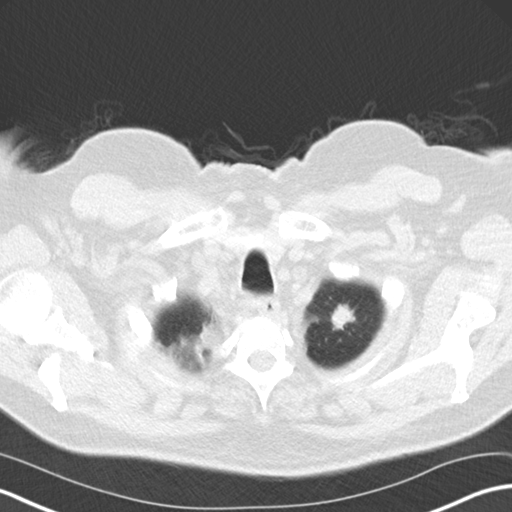
Axial slice from a low-dose chest CT screening exam. Third screening round (two years after baseline). Lung window (W 1500 / L -600 HU). 5 mm slice thickness. Standard (soft-tissue) reconstruction kernel (B30f). 512 × 512 image matrix. Male participant, aged 67 years at enrolment.
- Lesion marked by an expert reader, bounding box <323,299,360,338> (left, top, right, bottom; pixels).
- The exam's reader record, not a measurement of the box and not confirmed to be the same lesion: non-calcified nodule or mass ≥4 mm, left upper lobe, 20 × 15 mm, spiculated (stellate) margins, soft tissue attenuation, pre-existing on the prior screen: yes; interval growth: yes.
- Later outcome: lung cancer diagnosed 52 days after this screen — adenocarcinoma, NOS, left upper lobe, moderately differentiated (G2), stage IIA (AJCC 6th edition), 18 mm at pathology.